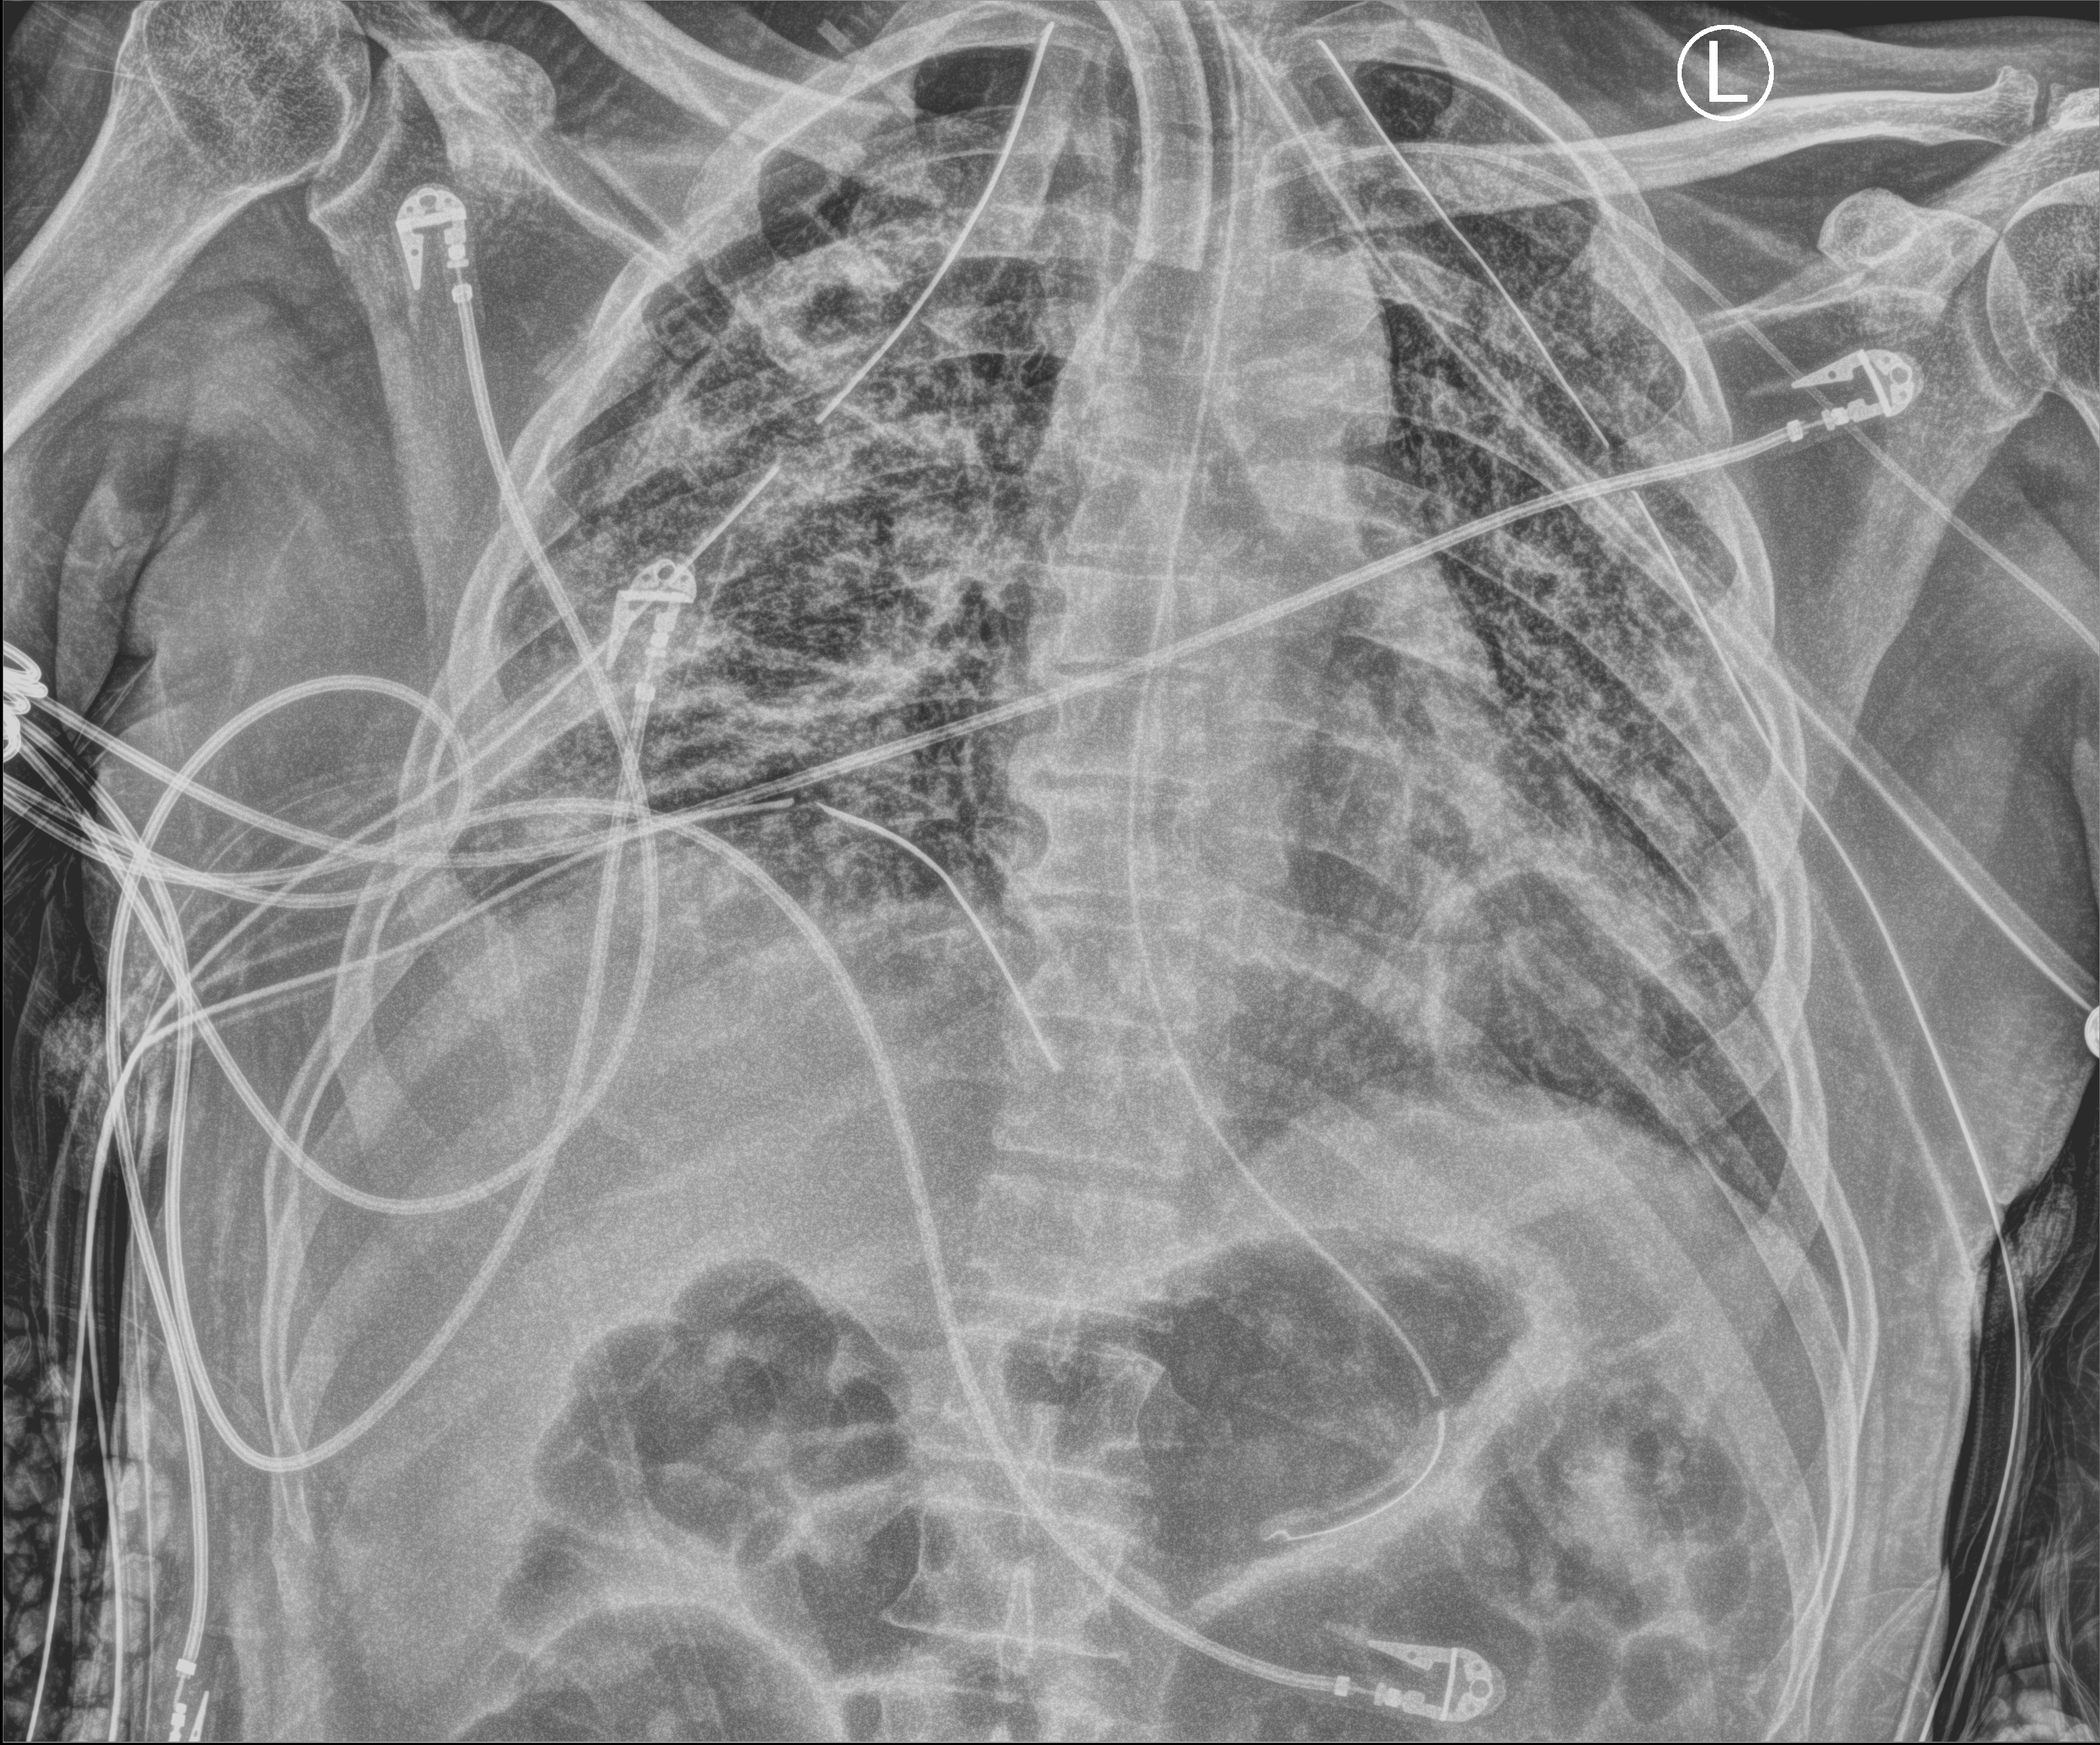
Chest X-ray (portable), anteroposterior (AP) projection. Patient hospitalised with COVID-19; male, aged 18–59 years.
Hospital-stay facts (about this admission, not read from this image; timing relative to this image not recorded):
- mechanically ventilated during this hospital stay: yes
- admitted to intensive care during this hospital stay: yes